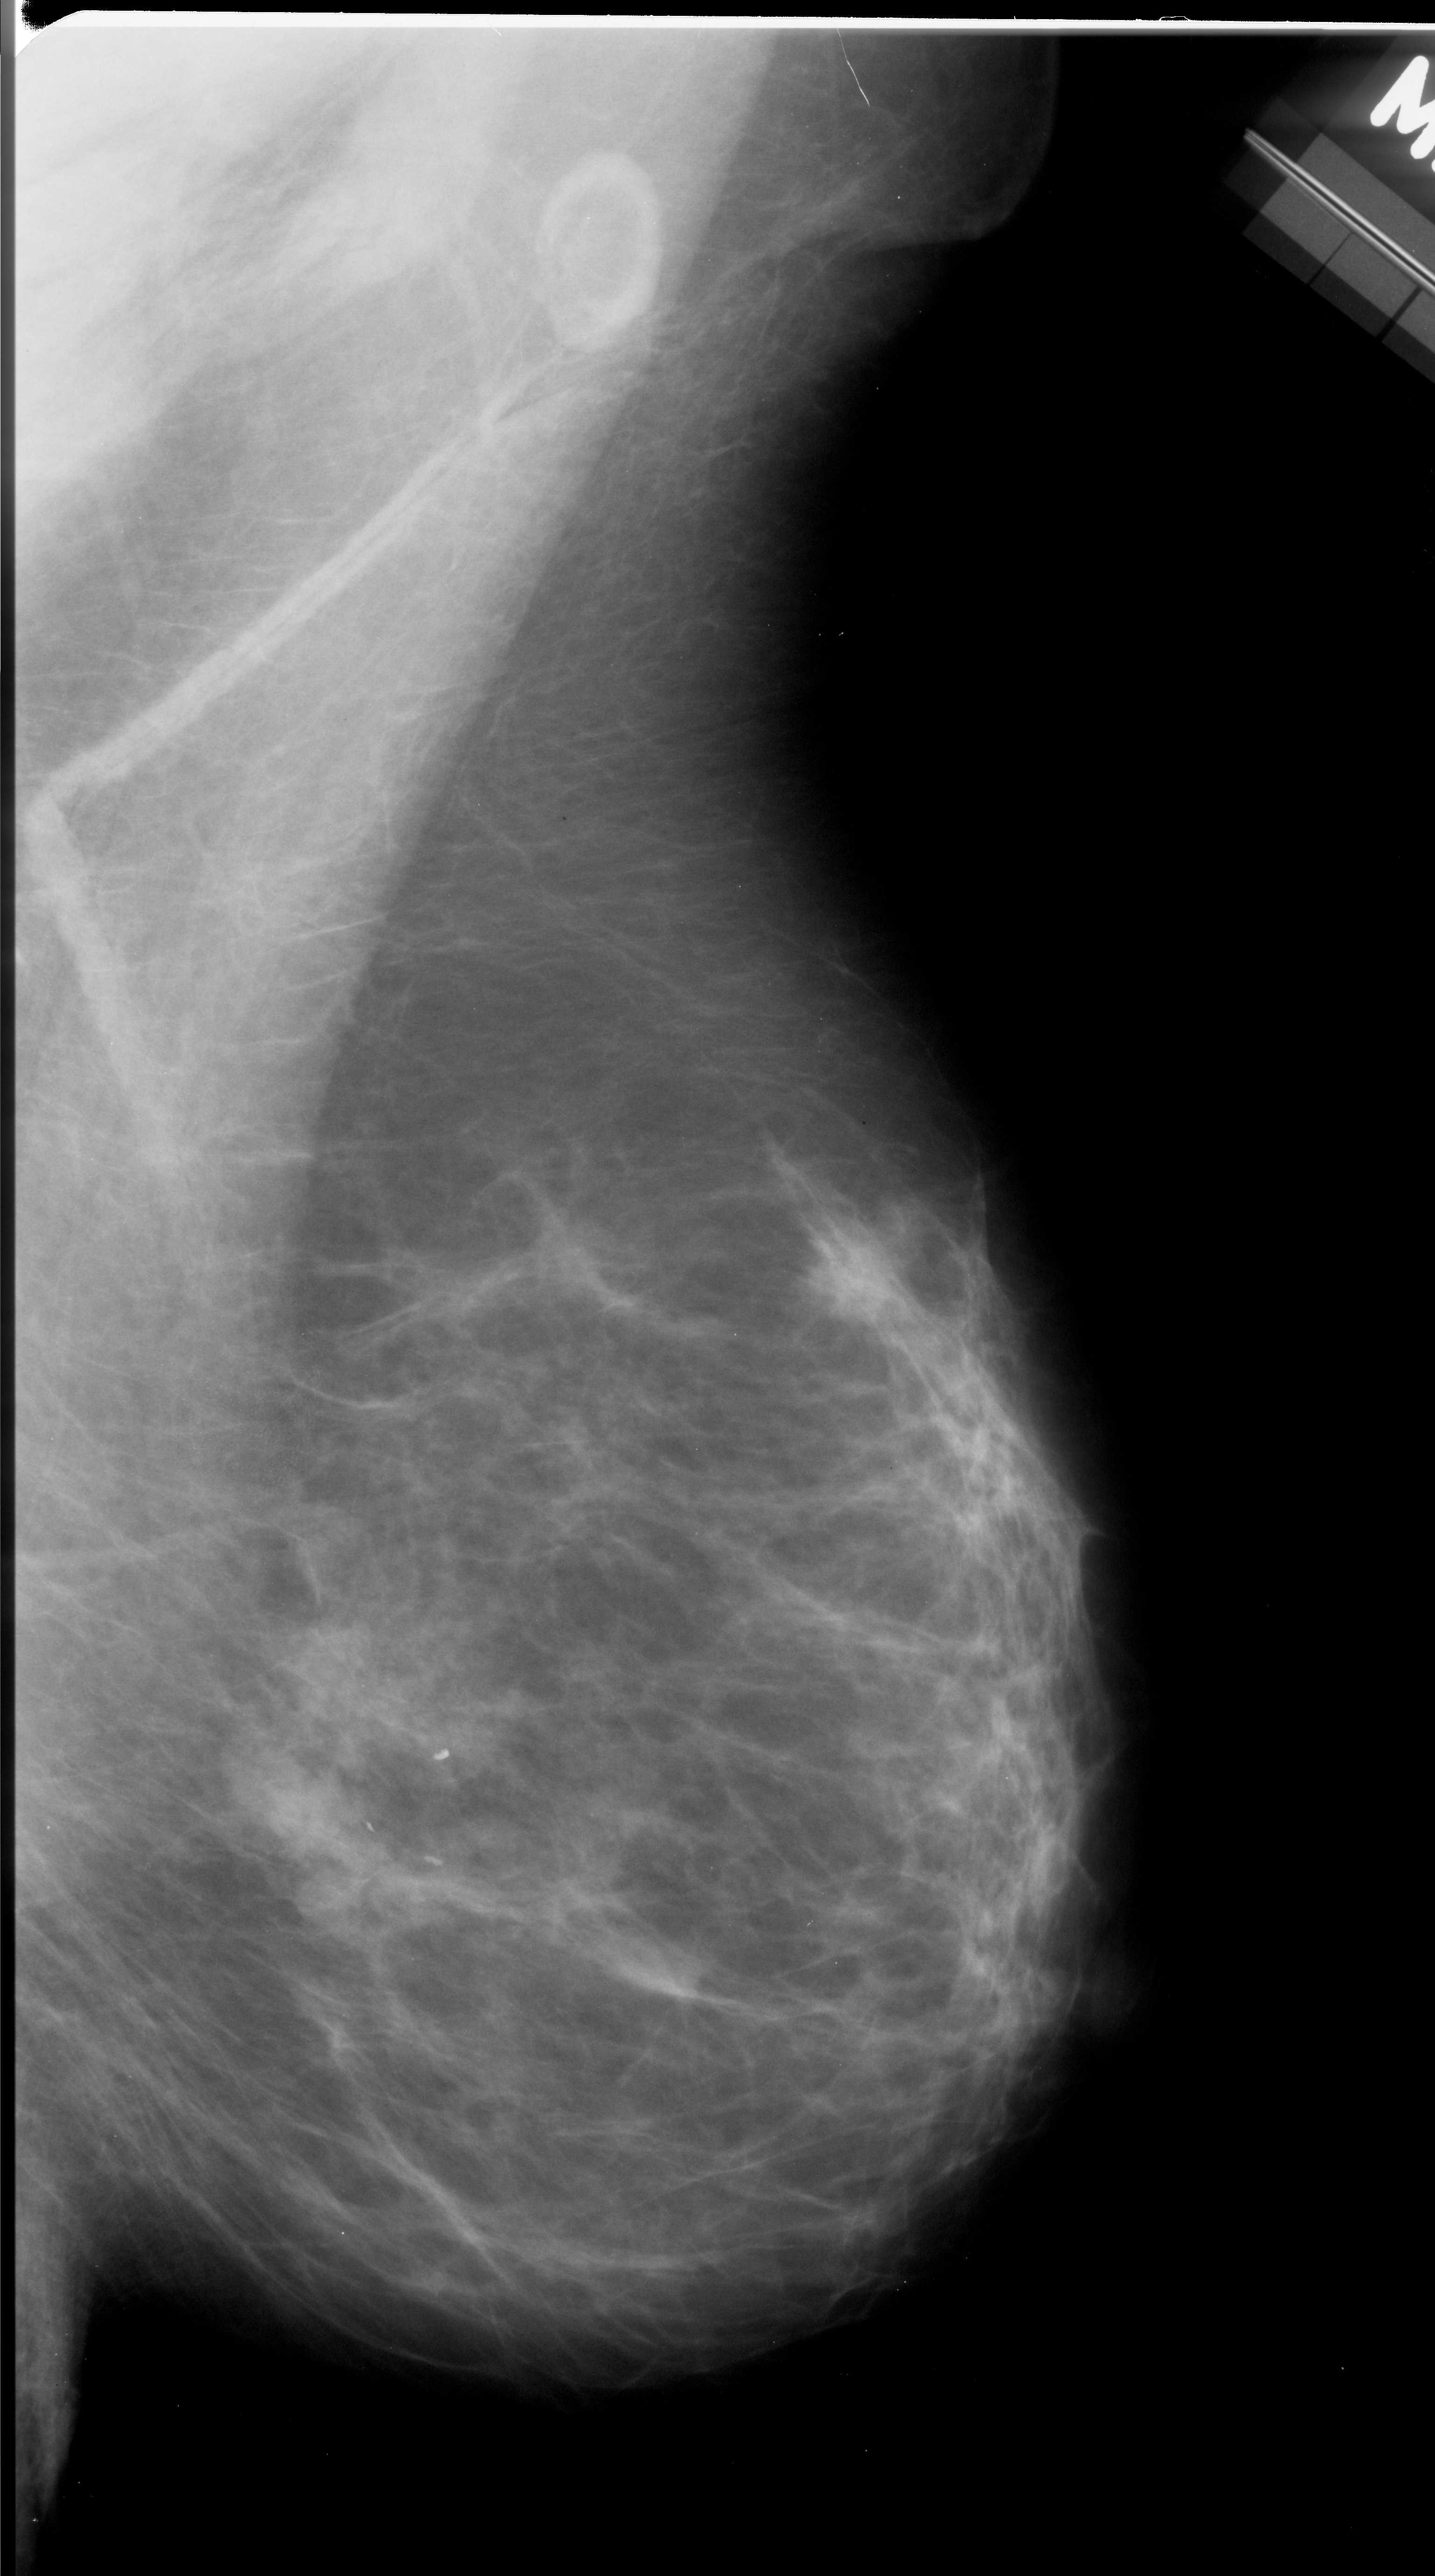
Mammogram (digitized film), right breast, mediolateral oblique (MLO) view, breast composition: scattered fibroglandular densities (BI-RADS density category 2 of 4).
- Marked findings (only marked abnormalities are described; nothing is implied about the rest of the image): mass, shape irregular, margins ill defined; BI-RADS assessment category 4; subtlety rating 5 on a 1 (subtle) to 5 (obvious) scale; pathology result (as recorded, not read from the image): malignant.